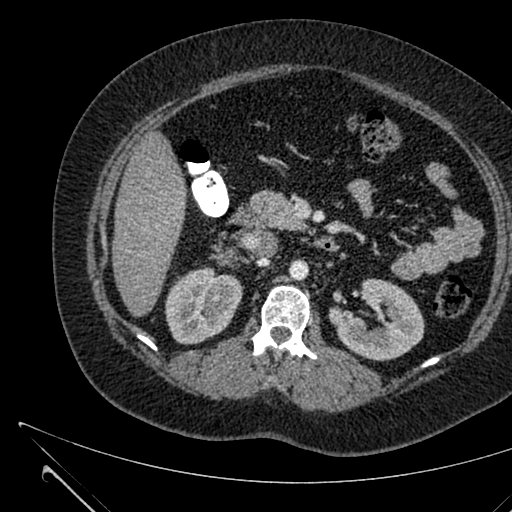
Contrast-enhanced abdominal CT, one axial slice. 120 kVp. Intravenous contrast given. Soft-tissue window (W 400 / L 40 HU). 512 × 512 image matrix, field of view 376 × 376 mm. Patient: female, 36 years. Case-level facts recorded for this patient, not image findings: diagnosis: adrenocortical carcinoma; tumour side: right adrenal; tumour size at pathology: 10 cm; Ki-67 index: 20 %; stage (as recorded): 4.
Structures marked on this image (semi-automatic segmentation, software-assisted and operator-edited):
- mass: bounding box <220,250,233,263> (left, top, right, bottom; pixels)